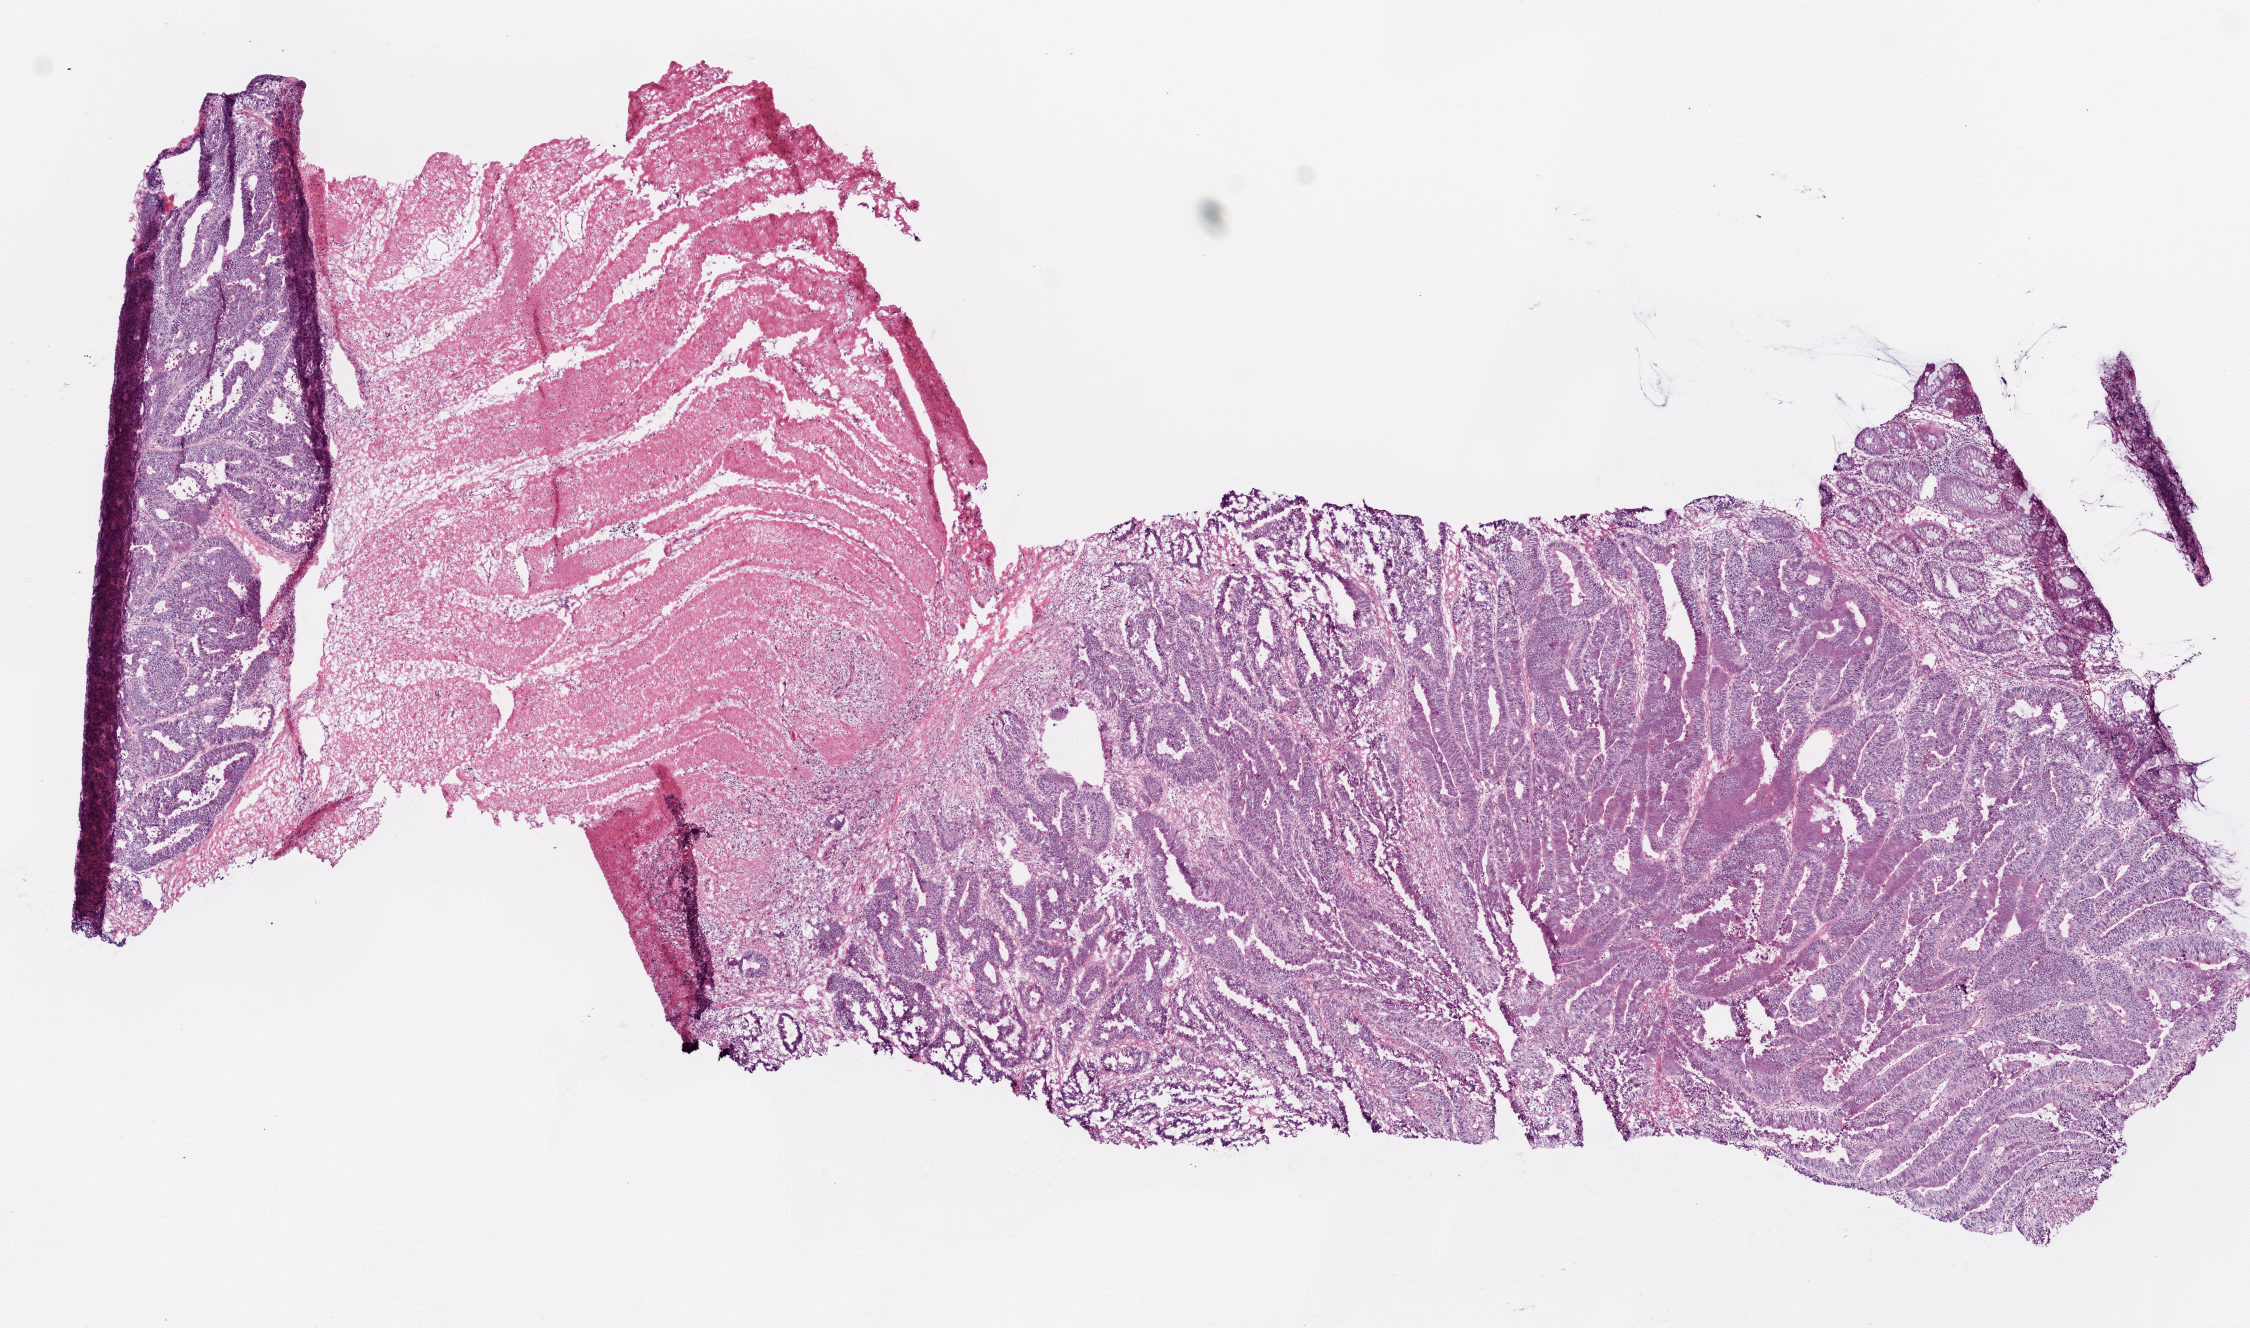
Digitized H&E tissue section (whole slide) — shown as a low-resolution overview of the whole scanned area (about 9.0 x 5.3 mm); frozen section from the top of the tissue portion; sample: primary tumour, colon. Male patient; age at initial diagnosis 87 years. Slide review estimates, as recorded: tumour cells 60%, tumour nuclei 80%, normal cells 0%, stromal cells 40%, necrosis 0%. Inflammatory infiltration, as recorded: lymphocyte infiltration 2%.
AJCC pathologic stage: II (5th edition). Lymph nodes positive (case pathology): 0 of 22 examined. Pathologic diagnosis: Adenocarcinoma, NOS.